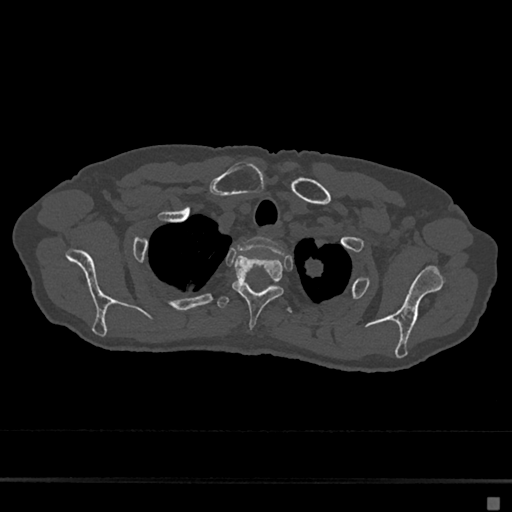
CT including the spine, one axial slice. Slice 572 of 797 in the series (ordered by position). Reconstruction kernel Br40s/3. Bone window (W 1800 / L 400 HU). 0.5 mm slice thickness. 512 × 512 image matrix, field of view 360 × 360 mm. Patient: female, 68 years. From the clinical record (not read from this slice): primary cancer: renal.
Annotated regions visible in this slice (semi-automatic segmentation, software-assisted and operator-edited):
- T1 vertebra: bounding box [x1, y1, x2, y2] px = [237, 236, 284, 254]
- T2 vertebra: [232, 255, 284, 327]
- T3 vertebra: [217, 296, 292, 313]